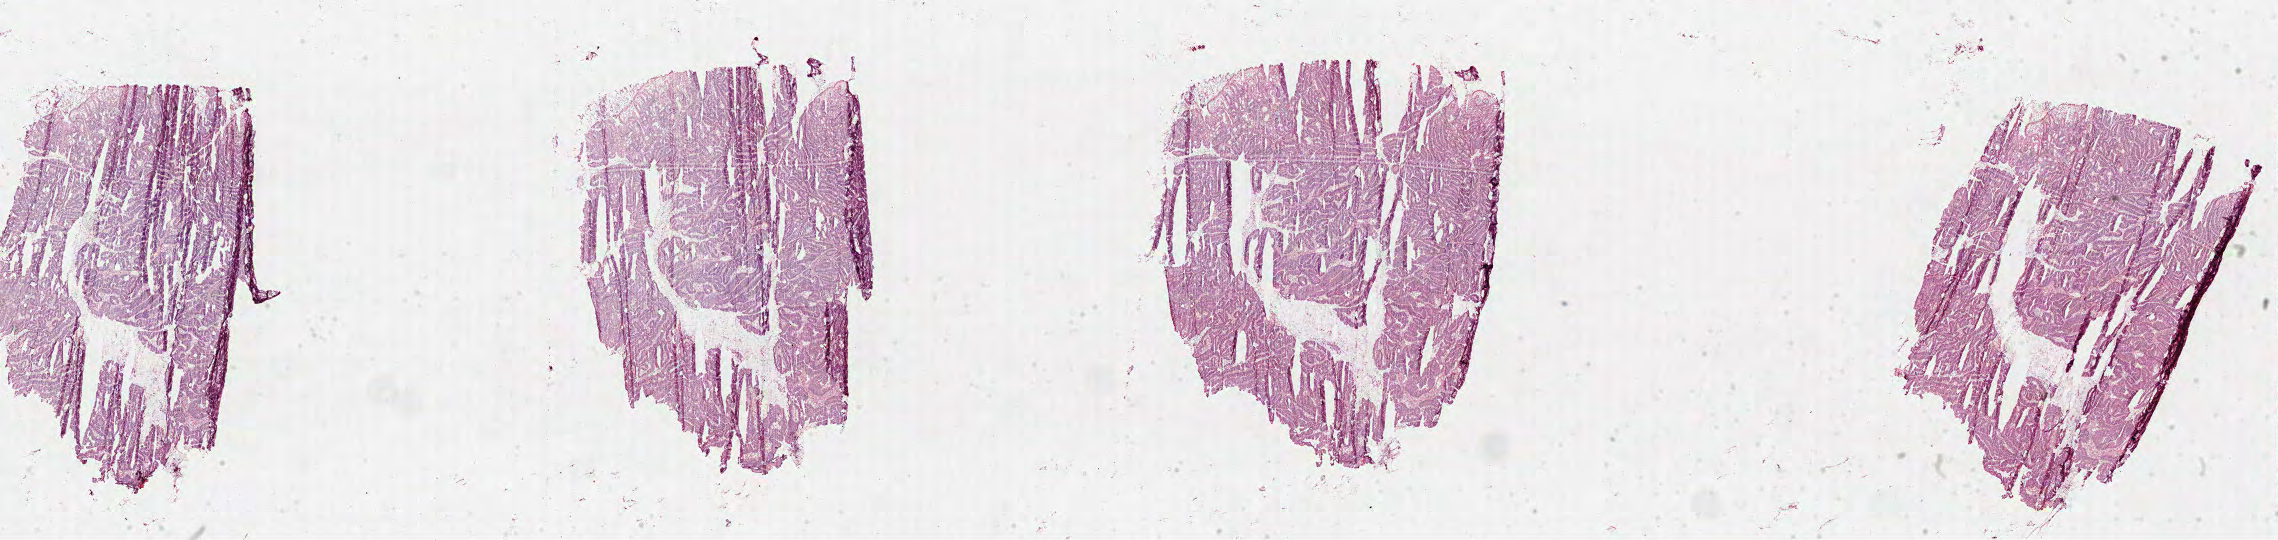
H&E whole-slide image — a low-resolution overview of the entire scanned area, about 36.7 x 8.7 mm (acquisition: 40x scan). Formalin-fixed paraffin-embedded (FFPE) diagnostic section. Sample: primary tumour, rectum. Male patient; age at initial diagnosis 59 years.
Lymph nodes positive (case pathology): 0 of 21 examined. Histologic diagnosis: Adenocarcinoma with mixed subtypes. AJCC pathologic stage: IIA (7th edition).